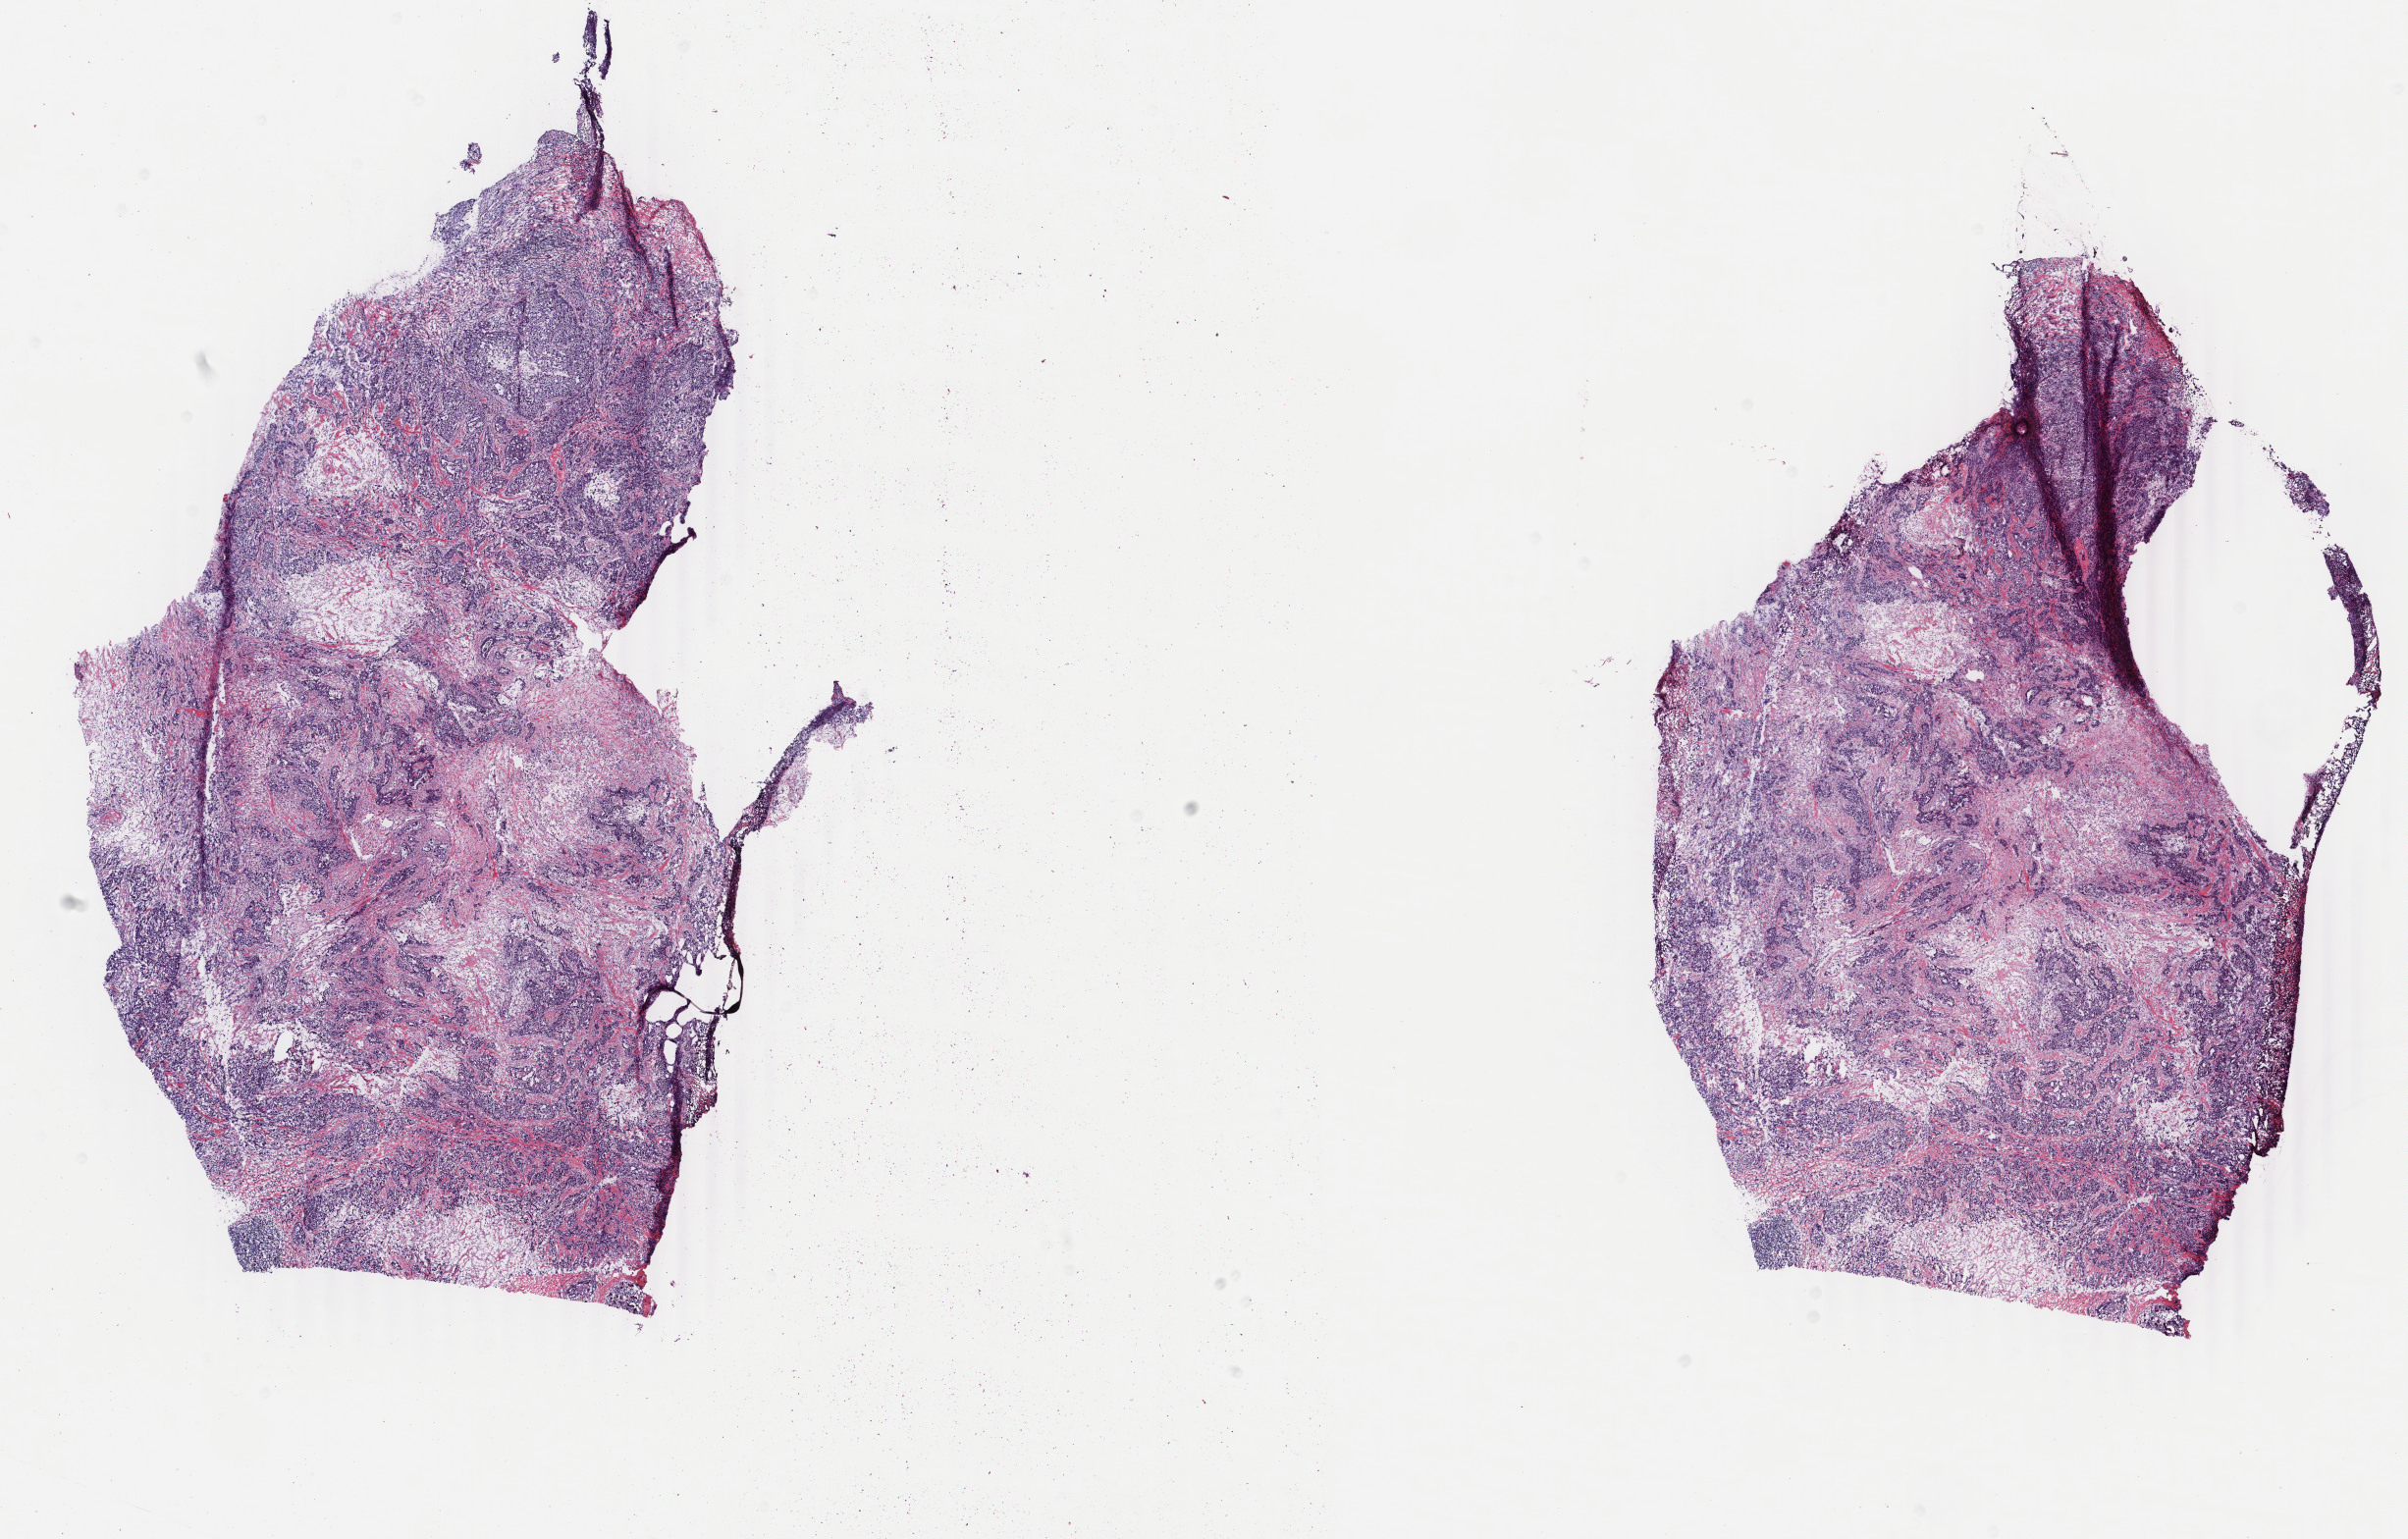
Whole-slide histology image, H&E, low-resolution overview of the scanned area, about 19.5 x 12.5 mm (from a 40x scan). Frozen section from the top of the tissue portion. Sample: primary tumour, breast. Female patient; age at initial diagnosis 41 years. Pathologist review of this section (percent, as recorded): tumour cells 80%, tumour nuclei 80%, normal cells 0%, stromal cells 19%, necrosis 1%. Infiltration values recorded for this section: lymphocyte infiltration 2%, monocyte infiltration 0%, neutrophil infiltration 0%.
Lymph nodes positive (case pathology): 0 of 4 examined. Histologic diagnosis: Infiltrating duct carcinoma, NOS. AJCC pathologic stage: IA.